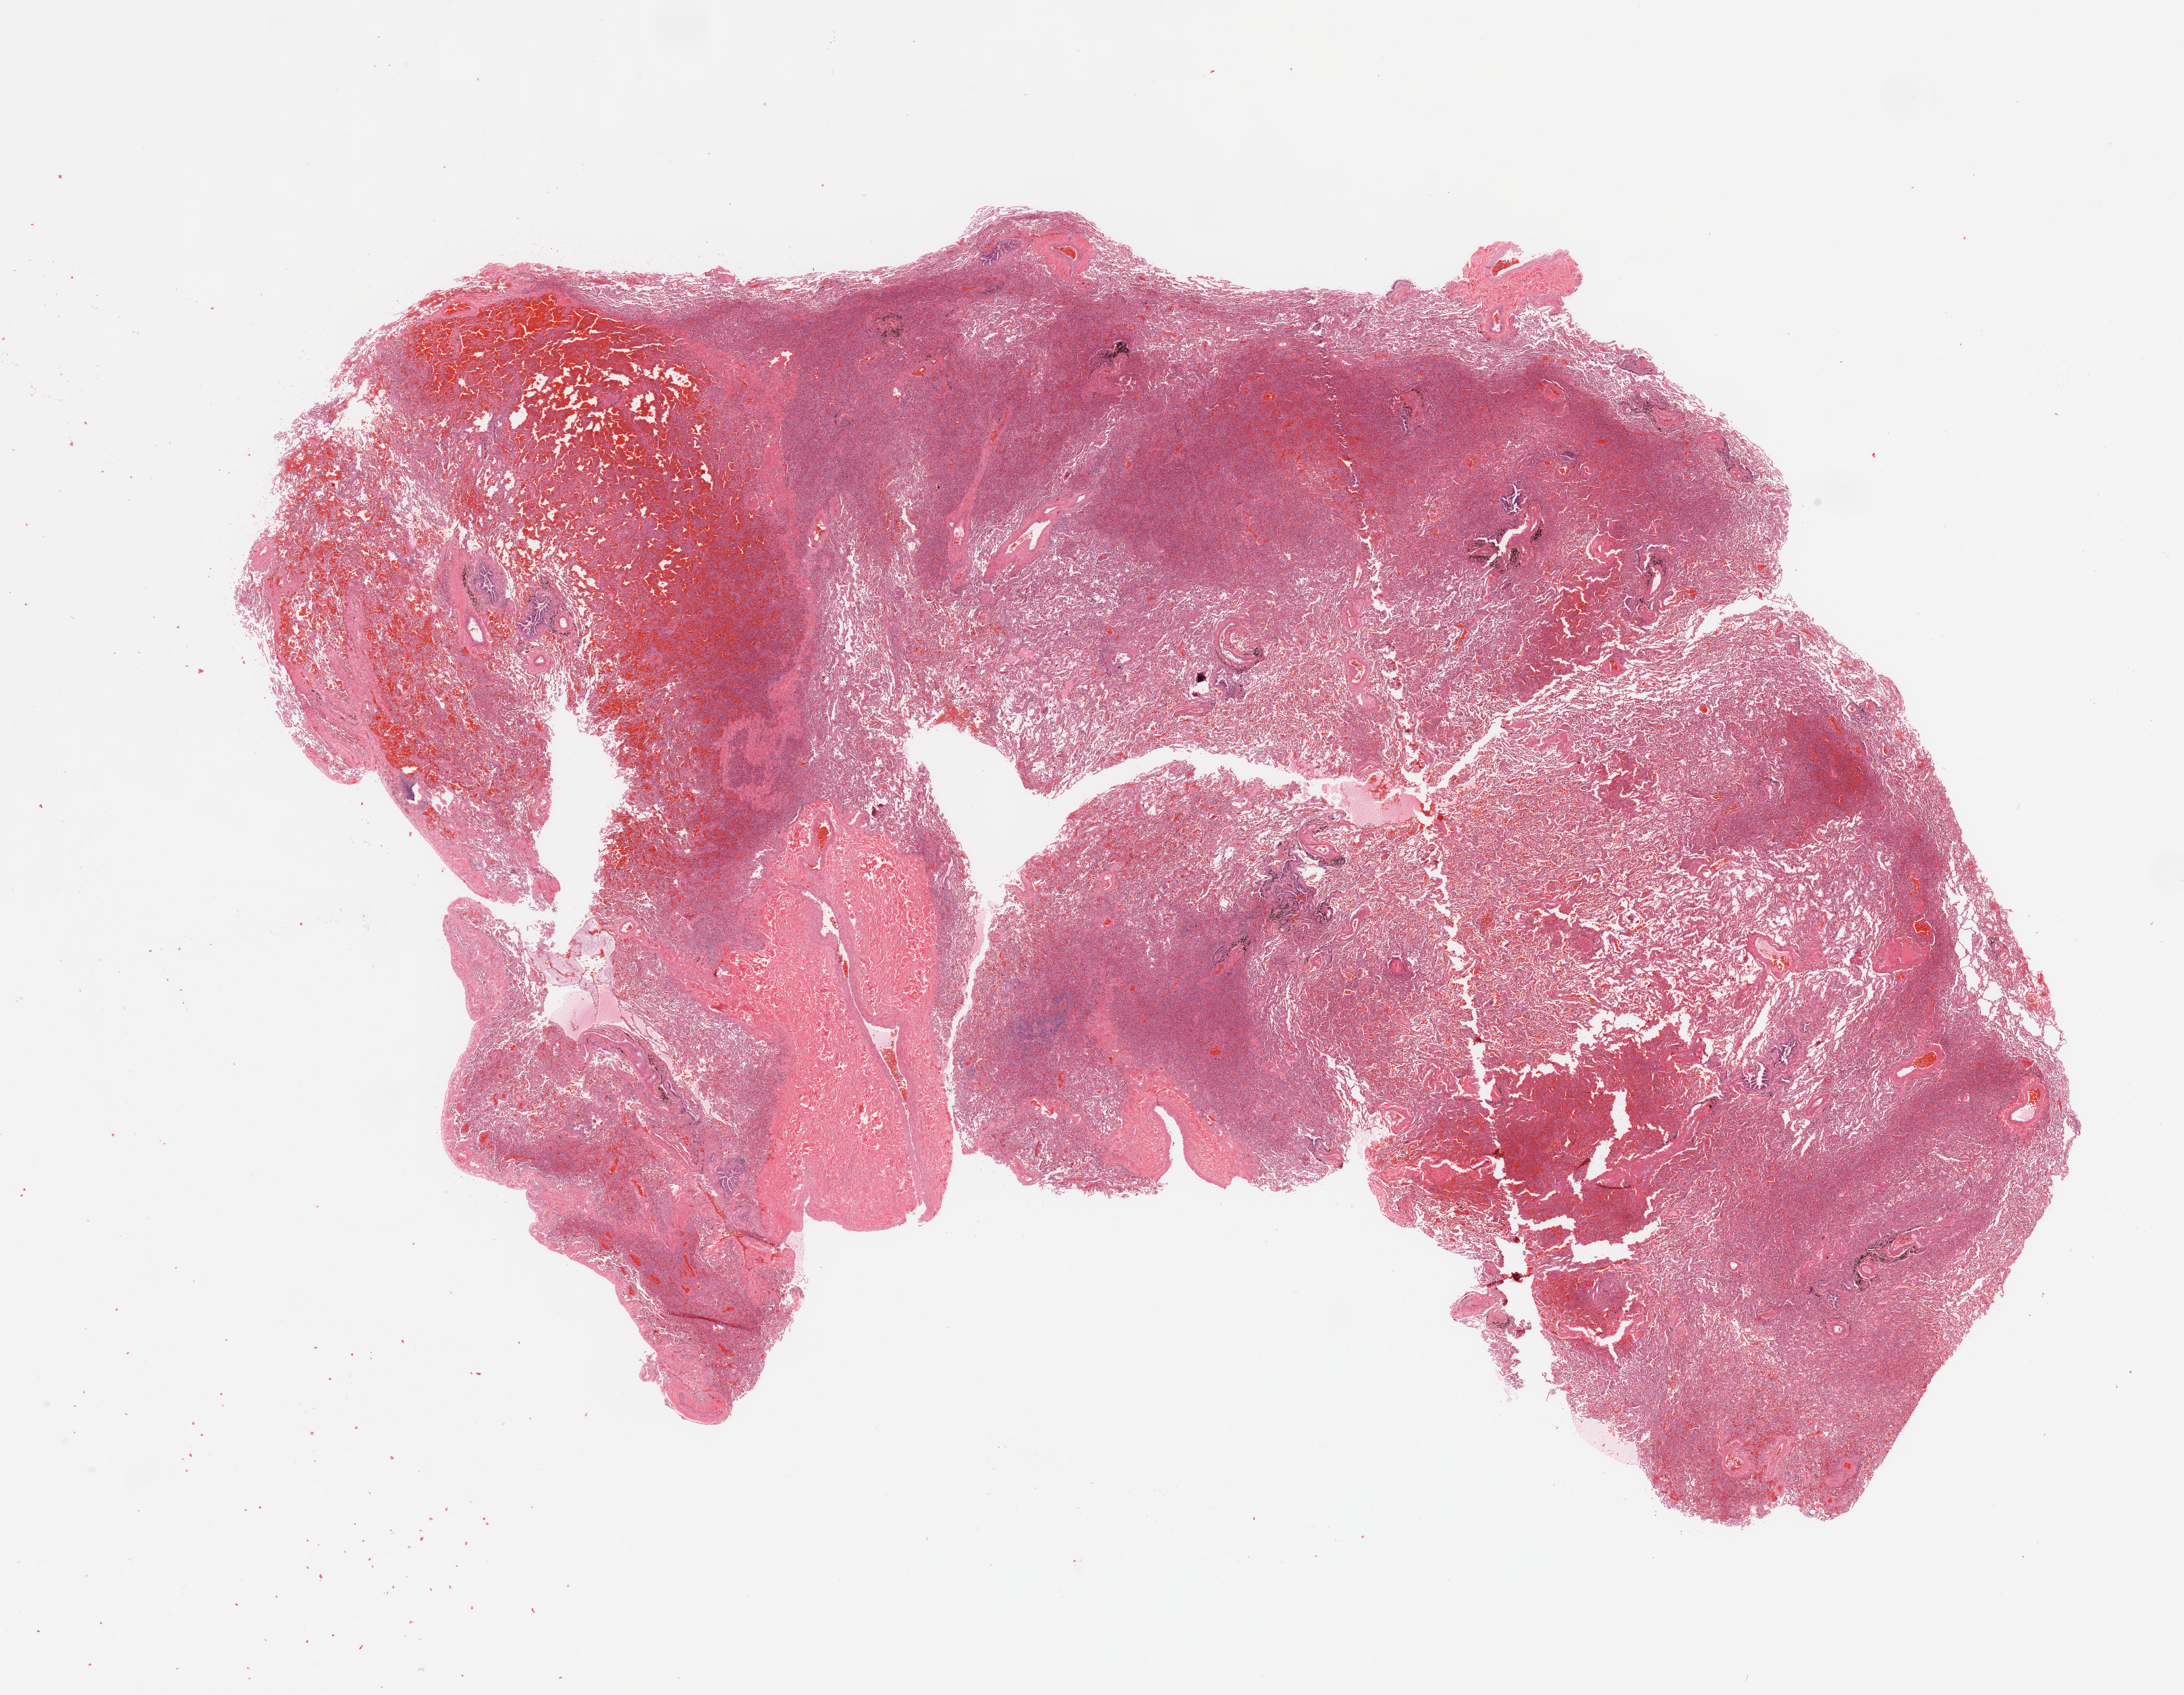
Whole-slide histology image, Hematoxylin and eosin (H&E) stained, shown as a low-resolution overview of the whole scanned area (about 25.6 x 19.9 mm, from a 20x scan); normal (non-tumour) tissue sample, sampled site: lung. 40-year-old male patient.
This section: normal (non-tumour) tissue from the same patient. Patient diagnosis: Adenocarcinoma, NOS.